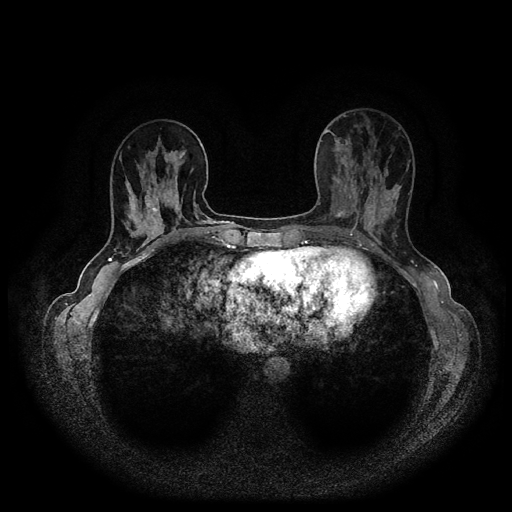
Breast MRI (dynamic contrast-enhanced, multi-phase), one axial slice. Position 36 of 116 along the scan axis. Dynamic contrast-enhanced series, time point 2 of 5 at this slice position (early post-contrast). 1.5 T. TE 2.6 ms, TR 5.4 ms. 2 mm slice thickness. 512 × 512 image matrix. Female patient, age 40 years.
Annotated regions visible in this slice (semi-automatically segmented with operator editing):
- breast lesion (labelled 'tumour' in the annotation; benign lesions carry a separate 'benign' label): bounding box (x1, y1, x2, y2) in pixels: (333, 208, 347, 218)